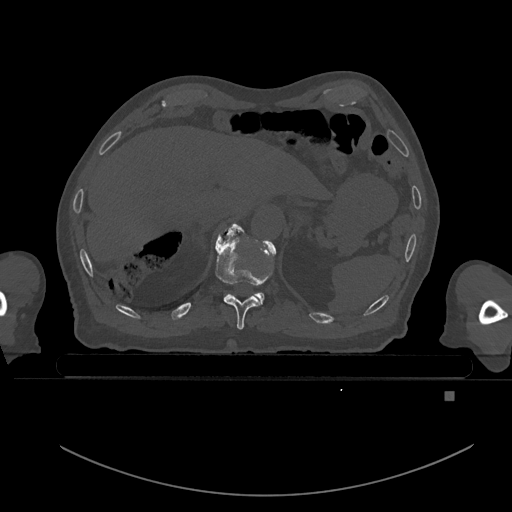
CT including the spine, one axial slice. Position 70 of 969 along the scan axis. Bone window (W 1800 / L 400 HU). 0.5 mm slice thickness. 512 × 512 image matrix, field of view 456 × 456 mm. Patient: male, 82 years. Case-level facts recorded for this patient, not image findings: primary cancer: prostate; vertebrae with lytic lesions (as recorded): T11, T9, T8, T2.
Structures marked on this image (semi-automatically segmented with operator editing):
- T10 vertebra: bounding box <215,224,273,330> (left, top, right, bottom; pixels)
- T11 vertebra: <220,225,273,304>